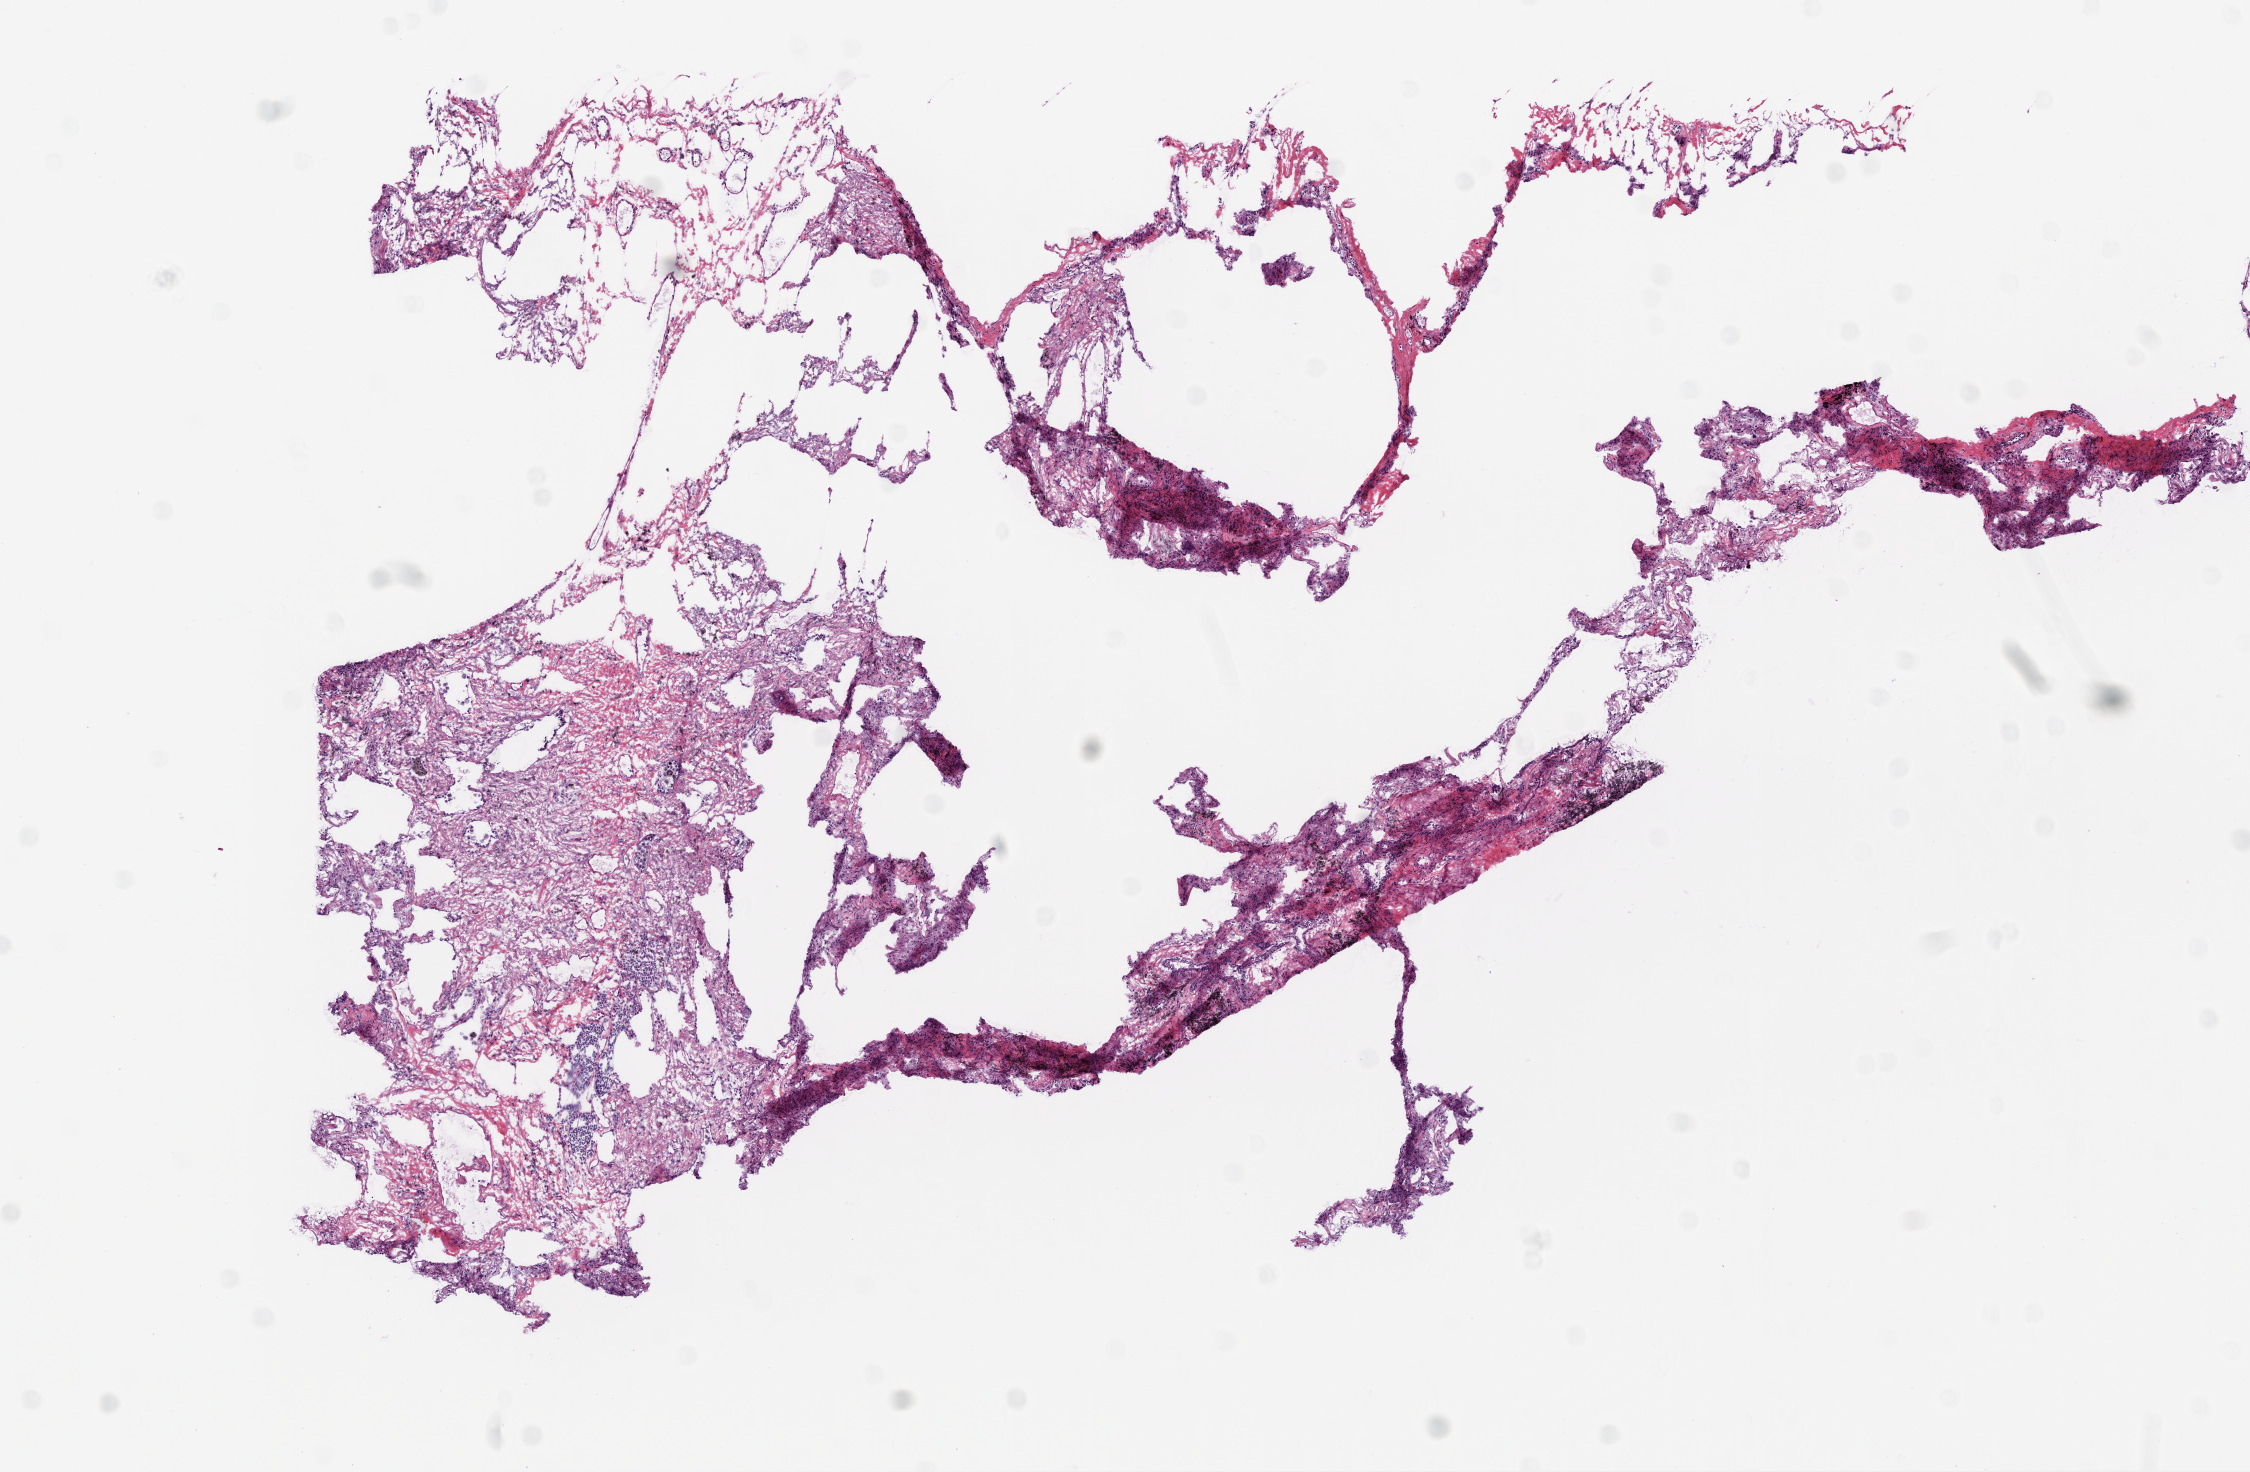
H&E-stained whole-slide image — a low-resolution overview of the entire scanned area, about 9.0 x 5.9 mm; frozen section; solid tissue normal (non-tumour tissue) sample from the lung. Male patient; age at initial diagnosis 65 years.
* this section: solid tissue normal sample (biorepository sample class)
* patient diagnosis: Squamous cell carcinoma, NOS (upper lobe, lung)